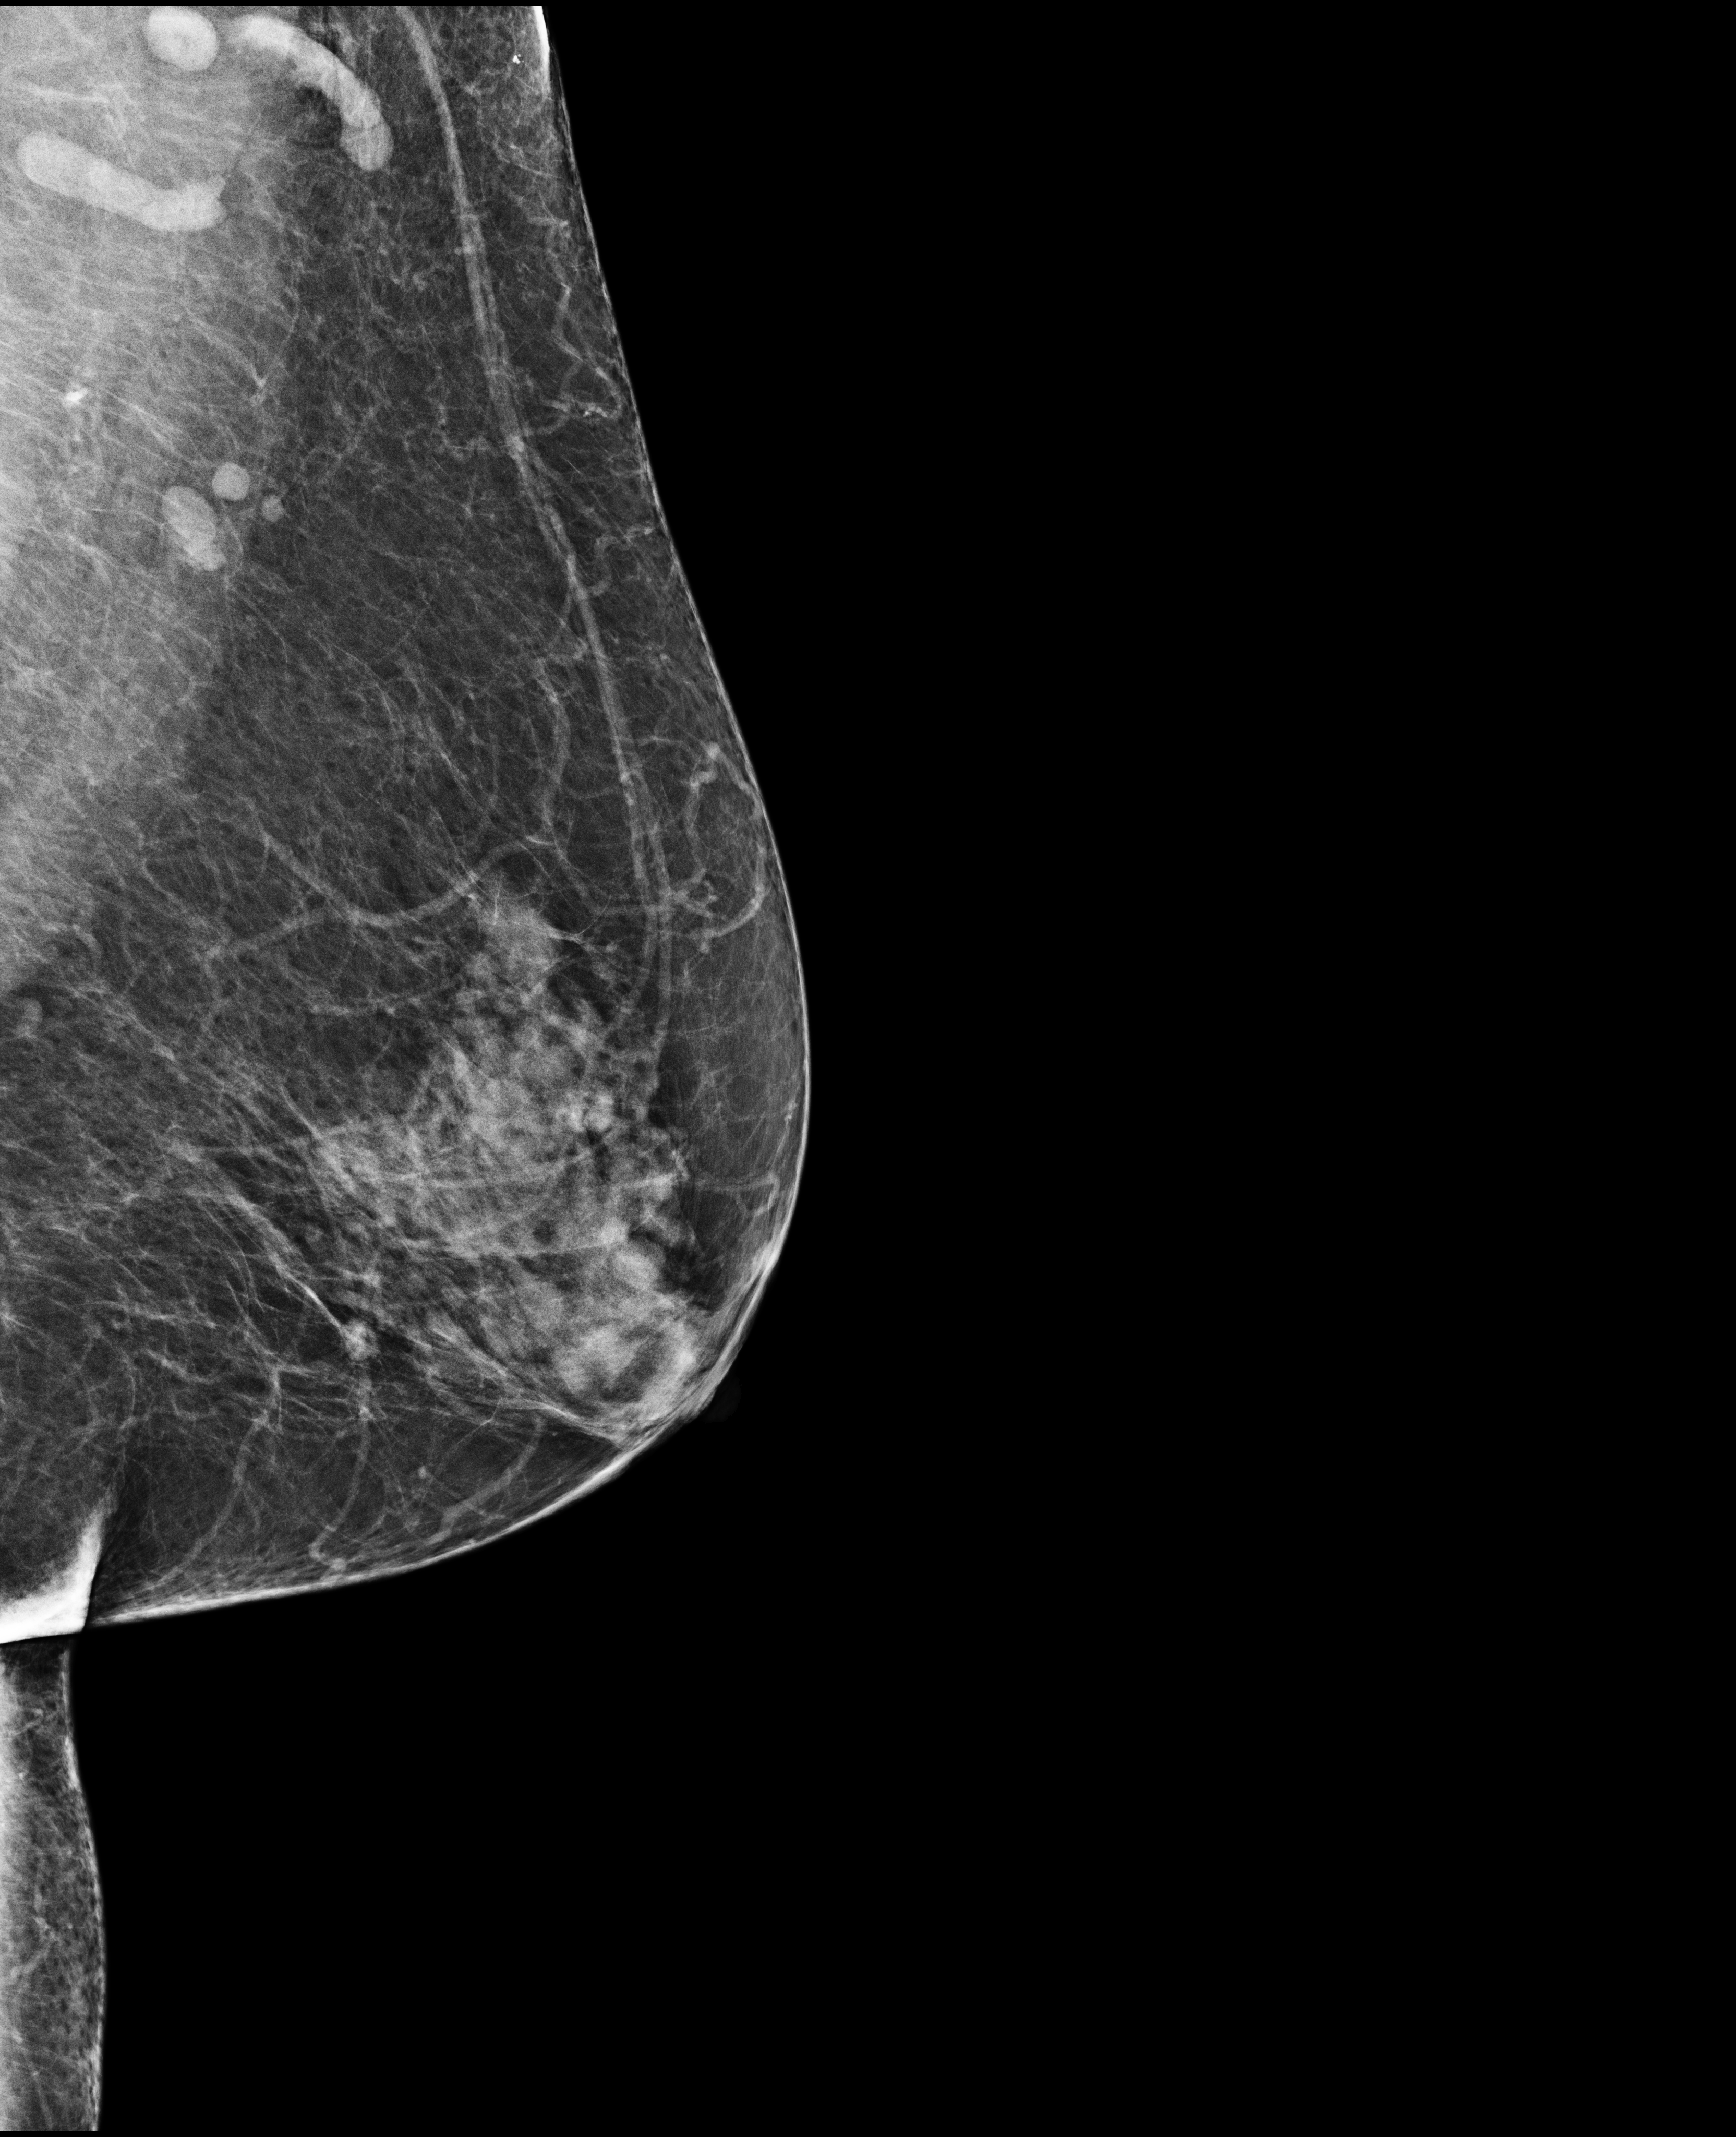
Annual screening mammography examination; system: Selenia Dimensions. Patient: female, 70 years.
Image type: full-field digital mammogram. Breast: left. Projection: mediolateral oblique (MLO) view.